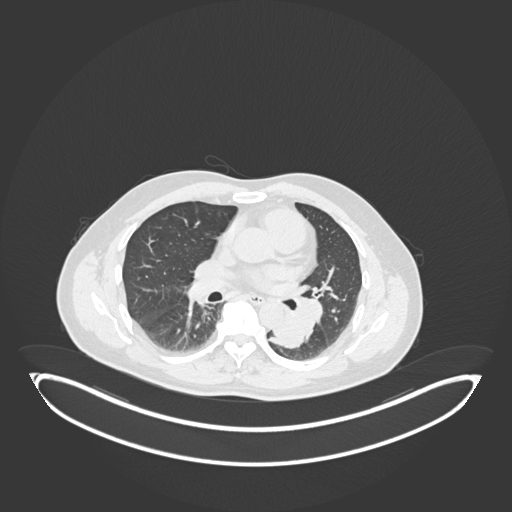
Chest CT, one axial slice; position 106 of 258 along the scan axis; lung window (W 1500 / L -600 HU); 1 mm slice thickness; 512 × 512 image matrix, field of view 500 × 500 mm. Patient: male, 54 years. From the clinical record (not read from this slice): clinical TNM (as recorded): T3 N0 M0.
Annotated regions visible in this slice (rectangle marked by the reading radiologist):
- lung tumour (recorded histology: squamous cell carcinoma): bounding box (x1, y1, x2, y2) in pixels: (266, 307, 305, 354)